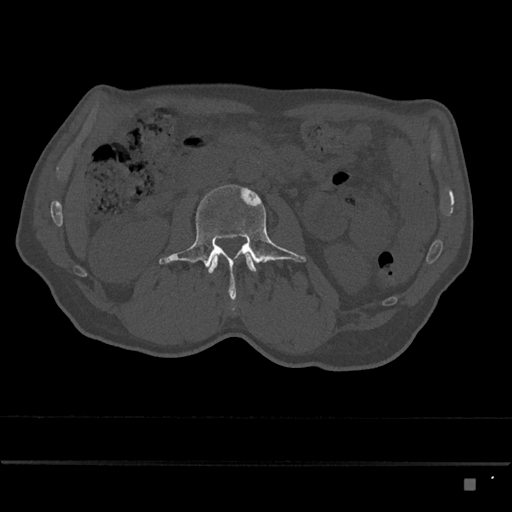
CT including the spine, one axial slice. Position 422 of 797 along the scan axis. 120 kVp. Bone window (W 1800 / L 400 HU). 0.5 mm slice thickness. 512 × 512 image matrix. Male patient, age 72 years. Case-level facts recorded for this patient, not image findings: primary cancer: prostate.
Annotated regions visible in this slice (semi-automatic segmentation, software-assisted and operator-edited):
- L2 vertebra: bounding box (x1, y1, x2, y2) in pixels: (208, 254, 257, 273)
- L3 vertebra: (159, 184, 306, 300)